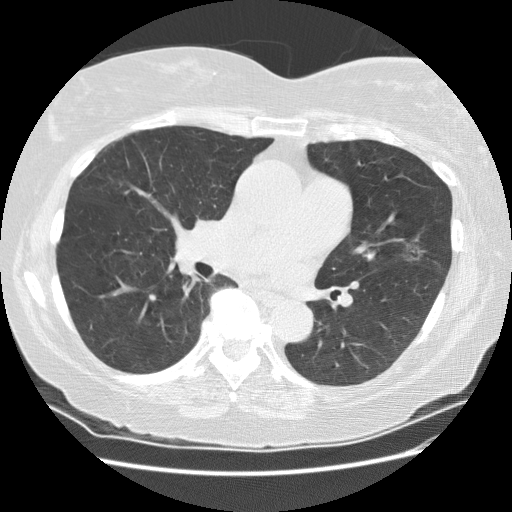
Low-dose screening chest CT, one axial slice. Slice 97 of 180 in the series (ordered by position). Reconstruction kernel STANDARD. 120 kVp. Lung window (W 1500 / L -600 HU). 2.5 mm slice thickness. 512 × 512 image matrix, field of view 360 × 360 mm.
Annotated regions visible in this slice (manually delineated by an expert):
- lesion 1 (tumor, upper lobe of left lung): bounding box [x1, y1, x2, y2] px = [403, 244, 427, 262]